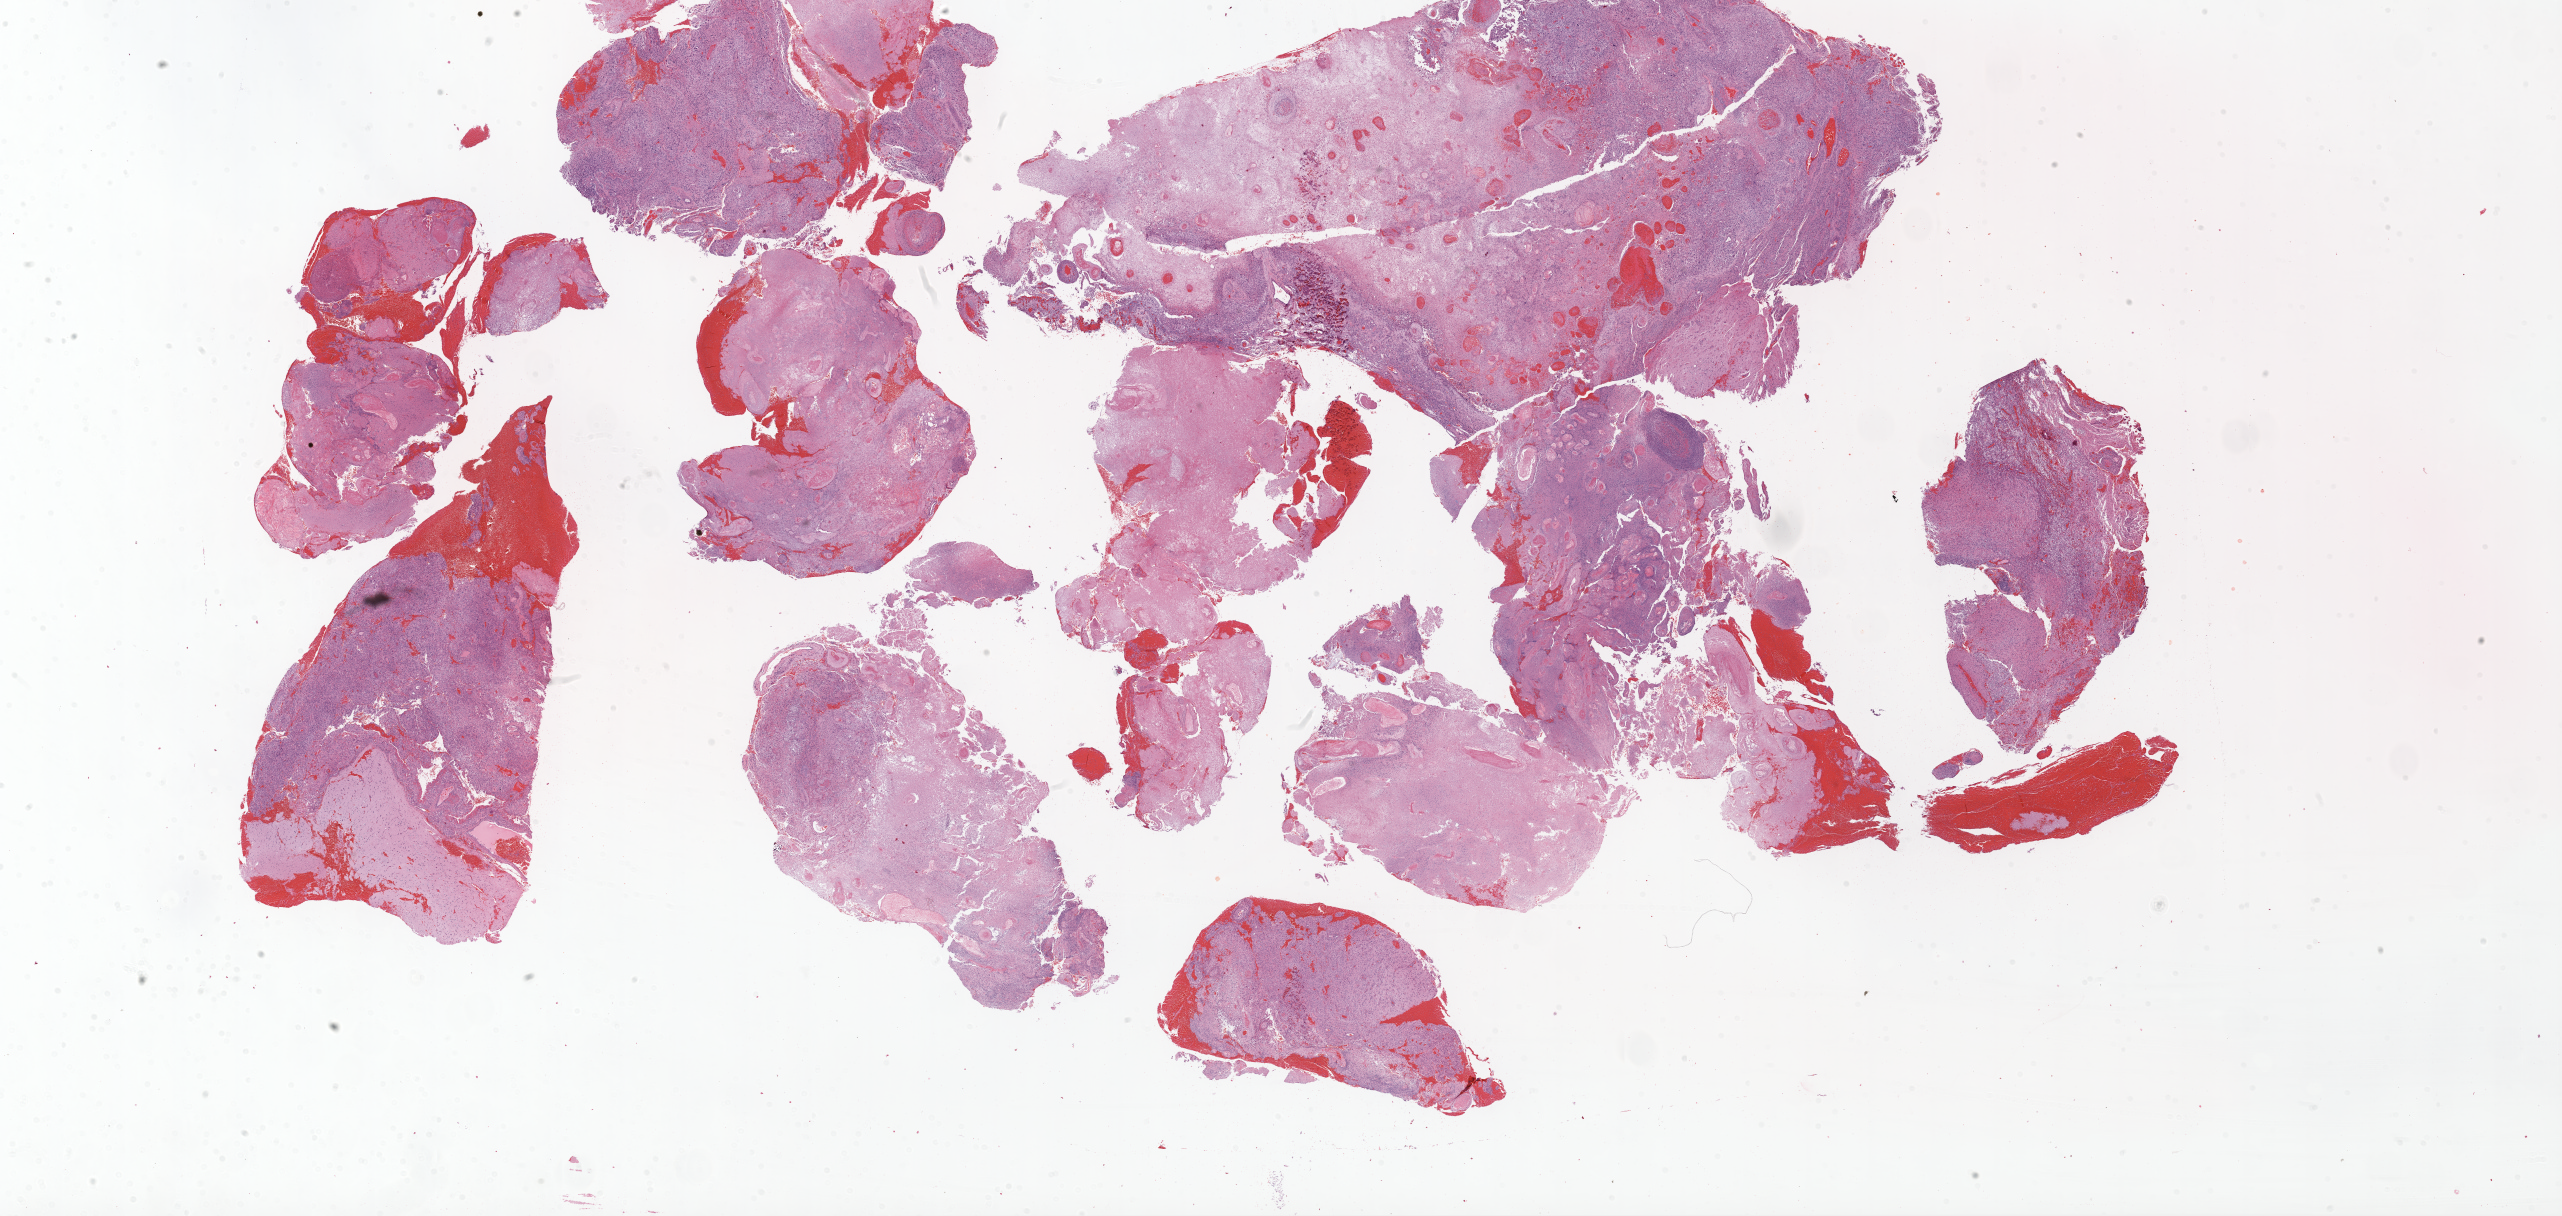
H&E whole-slide image — shown as a low-resolution overview of the whole scanned area (about 41.1 x 19.5 mm, slide scanned at 20x); formalin-fixed paraffin-embedded (FFPE) diagnostic section; primary tumour sample from the brain. Male, age 55 years at initial diagnosis.
Diagnosis: Glioblastoma.